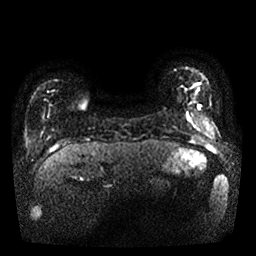
Breast MRI, one axial slice. Slice 2 of 25 in the series (ordered by position). Diffusion-weighted series; image 2 of 4 stored at this slice position (different b-values; order by instance number). 1.5 T. 4 mm slice thickness. 256 × 256 image matrix. Female patient.
Outlined on this slice (outlined manually by an expert reader):
- tumour on diffusion-weighted imaging: bounding box <185,113,191,123> (left, top, right, bottom; pixels)